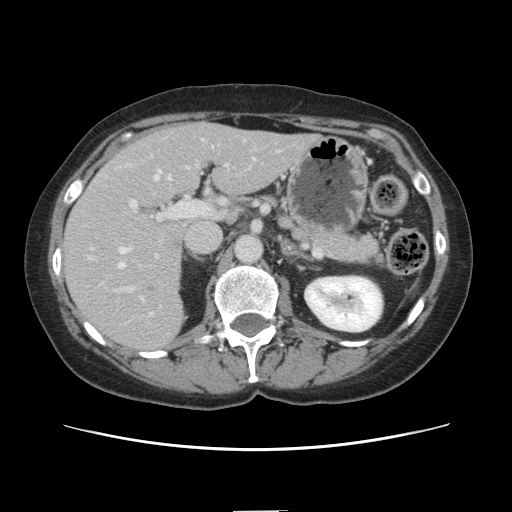
Contrast-enhanced abdominal CT, one axial slice. Position 76 of 141 along the scan axis. 120 kVp. Soft-tissue window (W 400 / L 40 HU). 2.5 mm slice thickness. 512 × 512 image matrix, field of view 350 × 350 mm. Female patient, age 63 years. Case-level facts recorded for this patient, not image findings: diagnosis: colorectal cancer liver metastases, imaged before liver resection; multiple liver metastases: yes; largest metastasis: 3.2 cm; disease in both lobes: yes.
Structures marked on this image (expert manual segmentation):
- hepatic veins: box from (x=89, y=171) to (x=170, y=269) px
- liver: (x=65, y=124)–(x=313, y=353)
- planned liver remnant (the part of the liver to remain after resection): (x=175, y=124)–(x=314, y=196)
- portal vein (with intrahepatic branches): (x=127, y=172)–(x=211, y=315)